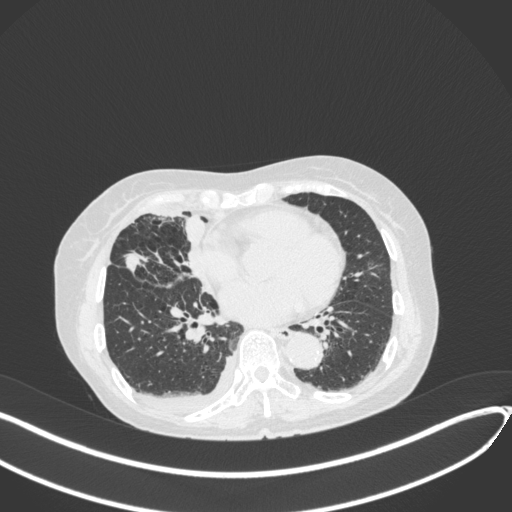
Chest CT, one axial slice. Reconstruction kernel B31f. 120 kVp. Lung window (W 1500 / L -600 HU). 512 × 512 image matrix, field of view 400 × 400 mm. Female patient, age 75 years. Case-level facts recorded for this patient, not image findings: clinical TNM (as recorded): T2a N3 M0.
Annotated regions visible in this slice (rectangle marked by the reading radiologist):
- lung tumour (recorded histology: adenocarcinoma): box from (x=123, y=246) to (x=145, y=275) px